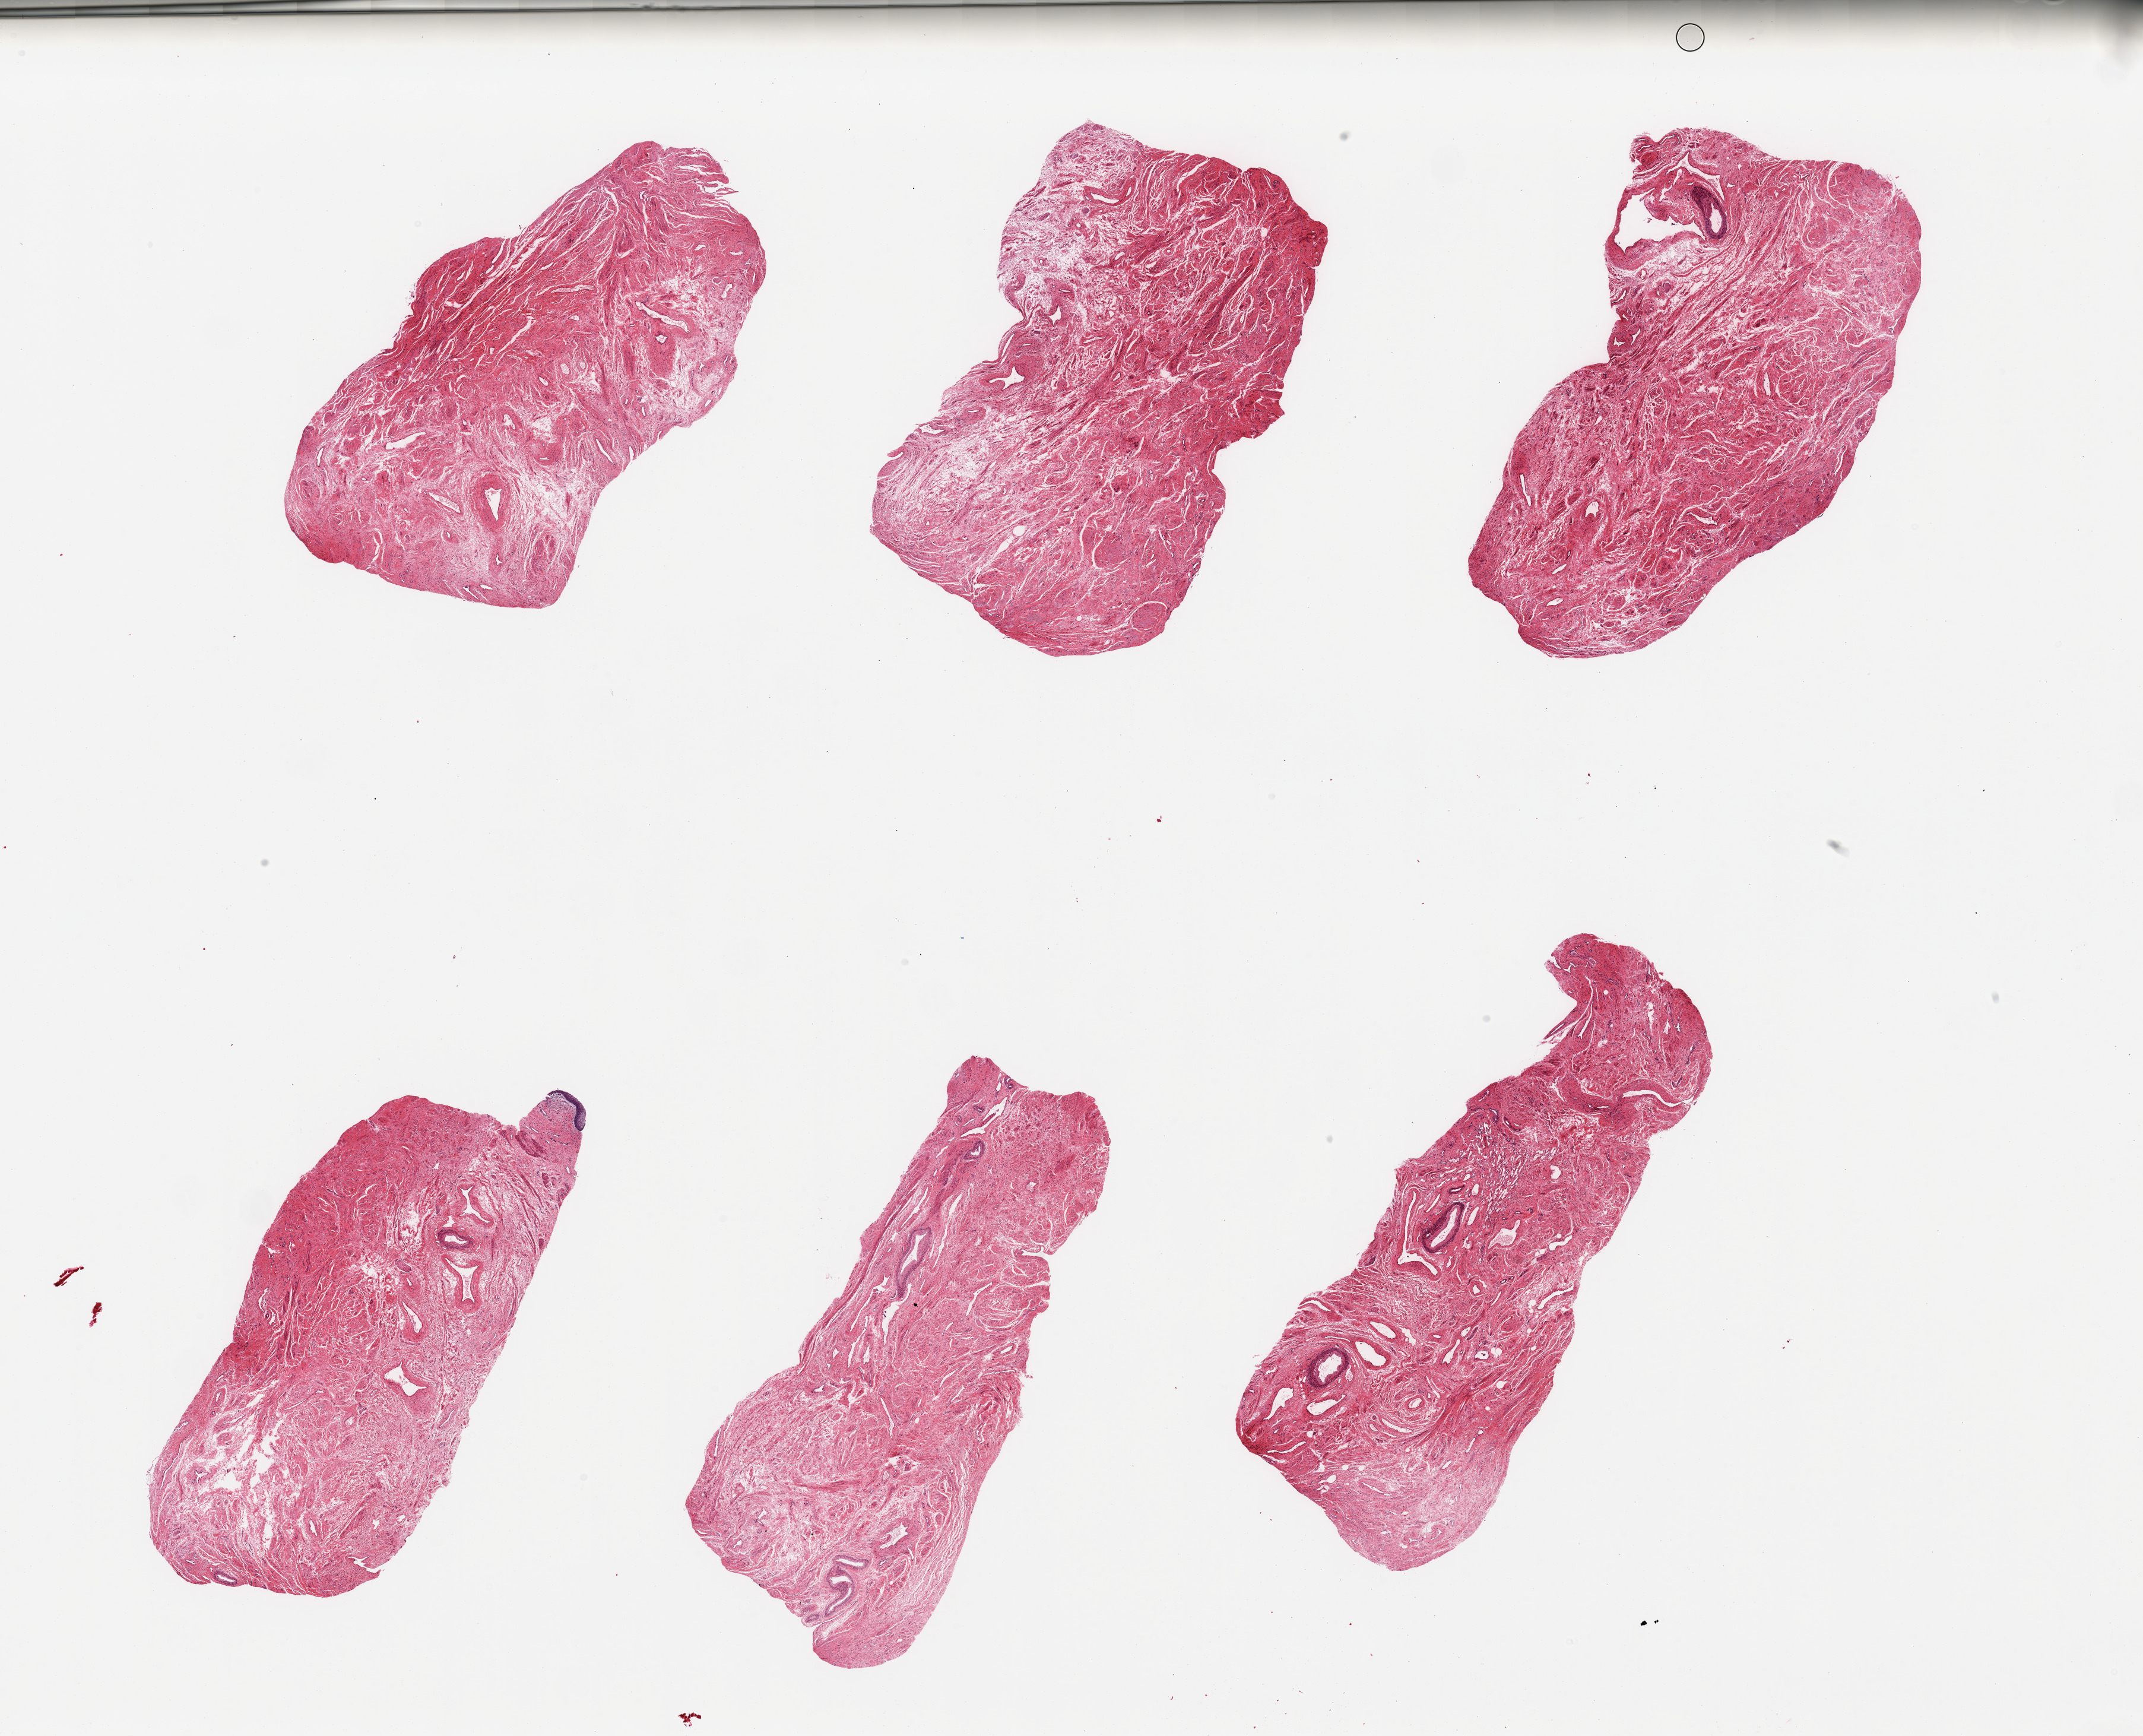
Whole-slide image, haematoxylin and eosin stain, a low-resolution overview of the entire scanned area, about 28.5 x 23.1 mm; PAXgene-fixed, paraffin-embedded tissue; sampled site (target tissue): vagina; tissue donor sample. Donor: female.
- review note (as recorded): 6 pieces; one piece contains tiny fragment of squamous epithelium; mostly fibromuscular tissue with vessels and small nerves